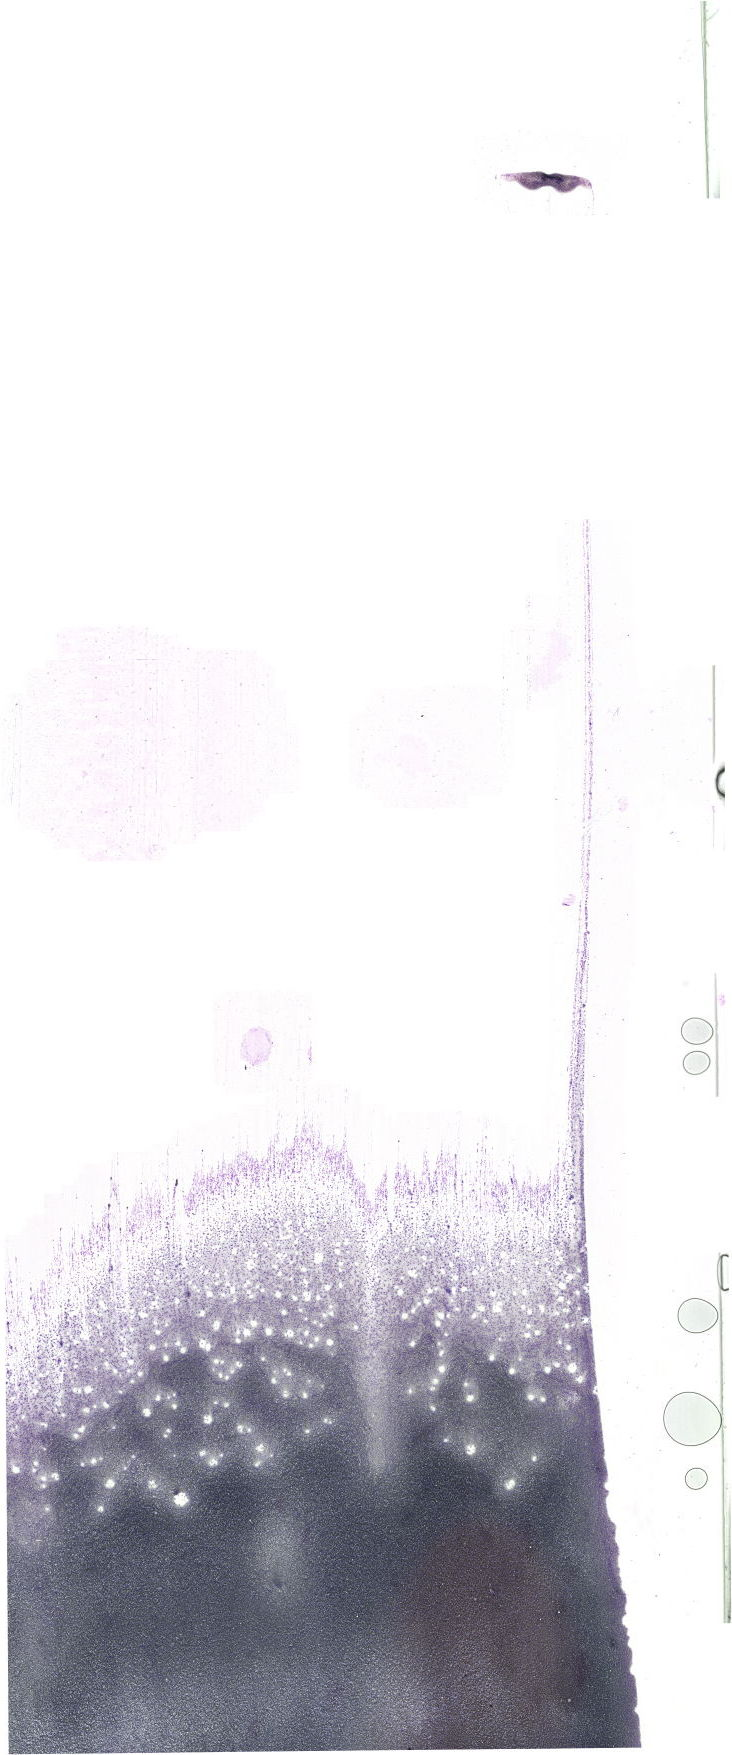
May-Grünwald–Giemsa-stained marrow aspirate smear (whole slide), low-resolution overview of the scanned area, about 20.7 x 49.7 mm. Male patient.
Diagnosis: Chronic Phase Chronic Myeloid Leukemia, BCR-ABL1 Positive.